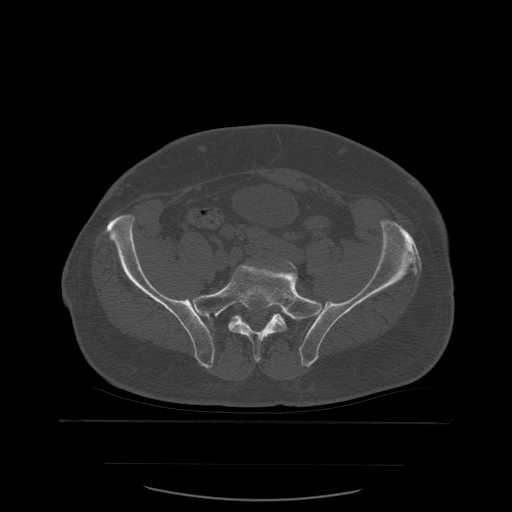
CT including the spine, one axial slice. Slice 114 of 590 in the series (ordered by position). Bone window (W 1800 / L 400 HU). 512 × 512 image matrix, field of view 479 × 479 mm. Patient age 71 years. From the clinical record (not read from this slice): primary cancer: lung; vertebrae with lytic lesions (as recorded): T1, T2, L5, S1.
Outlined on this slice (semi-automatic segmentation, software-assisted and operator-edited):
- L5 vertebra: box from (x=255, y=260) to (x=298, y=358) px